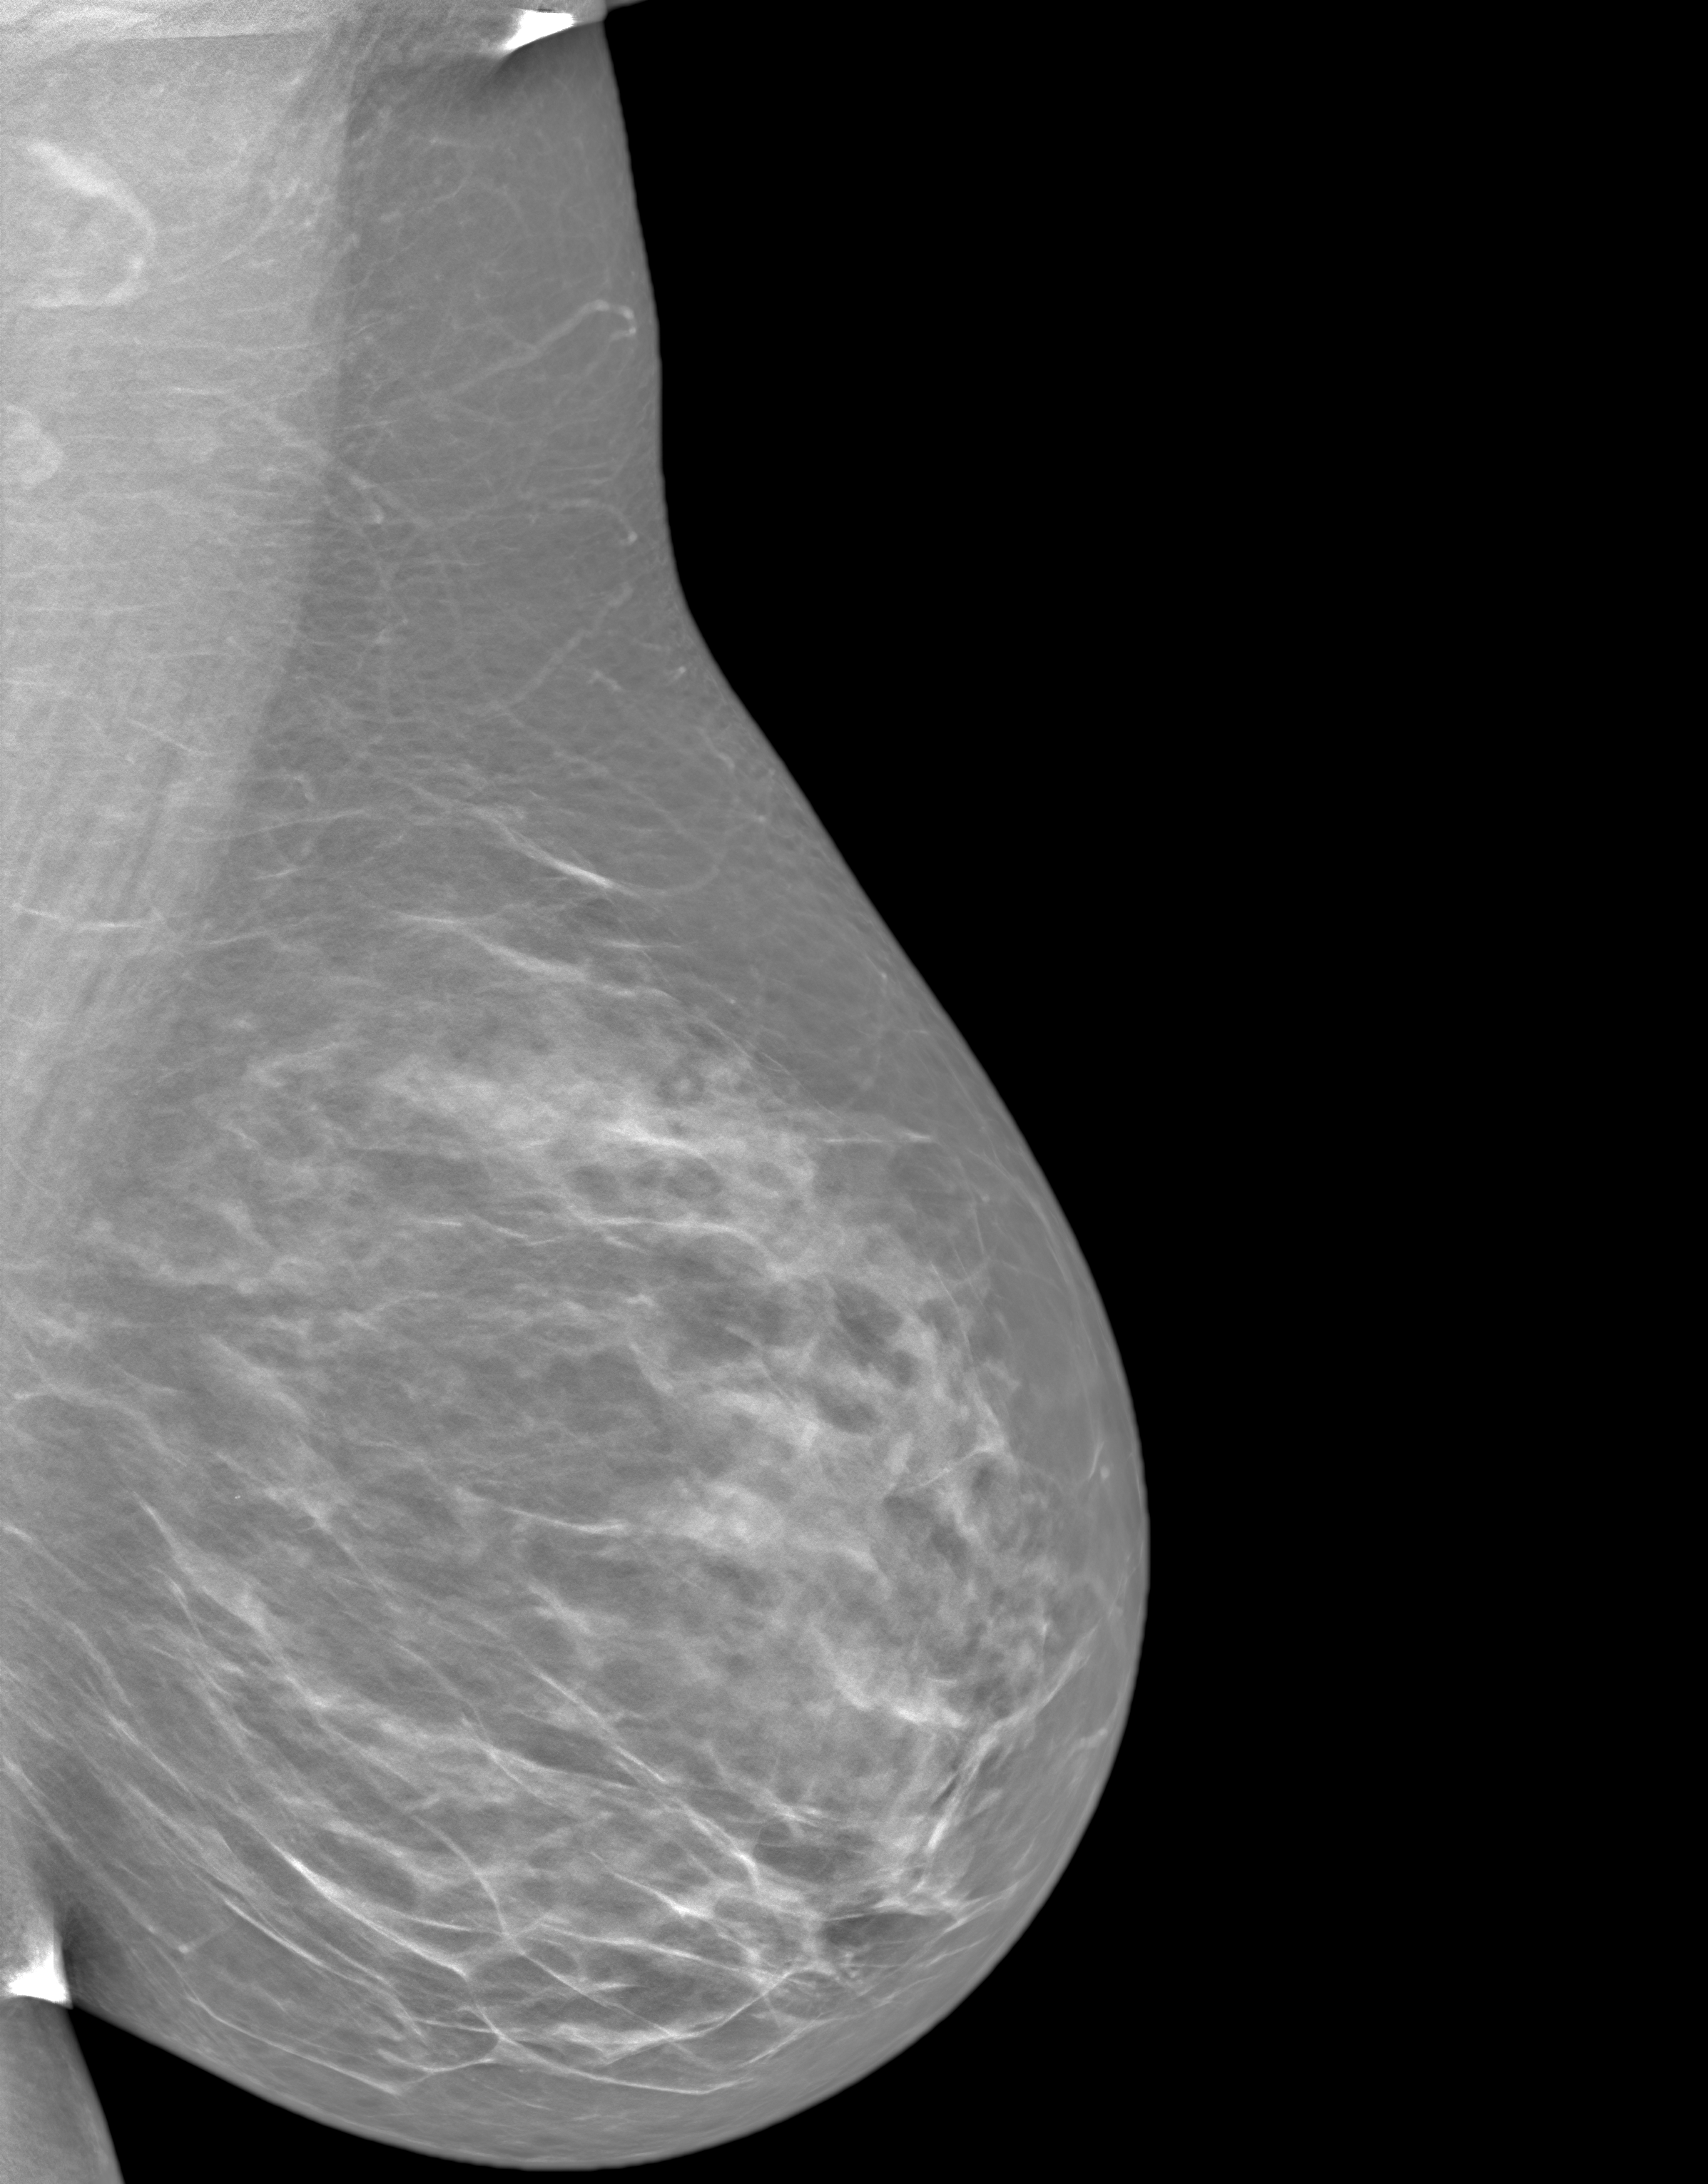
Annual screening mammography examination. Patient: female, 43 years.
Image type: synthesized 2-D view from tomosynthesis. Breast: left. Projection: MLO view.